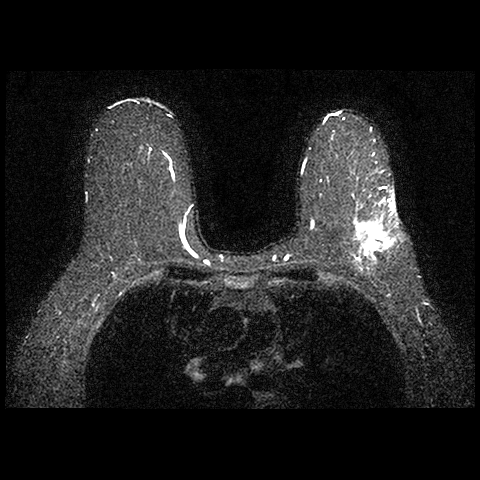
Breast MRI examination; 2 images, each one mid-volume slice chosen by position. Patient in her 70s.
Image 1: fluid-sensitive (T2/STIR) axial slice, slice 43 of 84, 2 mm slice thickness.
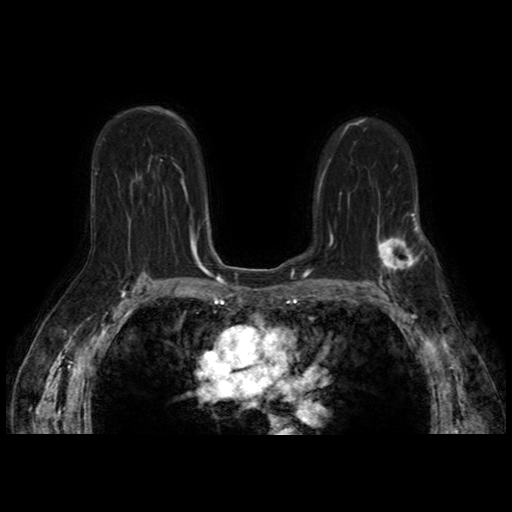
Image 2: post-contrast dynamic axial slice, series "AX BLISS_AUTO SENSE", slice 43 of 84, dynamic phase 6 of 10, 4 mm slice thickness.
MRI impression (as recorded): LEFT BREAST: There is minimal background enhancement. A mass in the left upper outer posterior breast has irregular margins with peripheral irregular enhancement and has associated mild architectural distortion. It is located at 2 o'clock , approximately 10 cm from the nipple and 2.2 cm from the chest wall. The mass demonstrates rapid intense early contrast enhancement with washout. It measures approximately 2.8 x 2.3 x 2.4 cm (Series 705, Slice 84). A biopsy clip is noted in the lateral portion of the mass. Two satellite foci of enhancement are noted adjacent to the known cancer with washout kinetics. One measures approximately 0.6 x 0.4 x 0.7 cm (Series 705, Slice 66), and is located approximately 1 cm inferior to the large mass in the left upper outer breast at 2 o'clock, approximately 10 cm from the nipple. The other focus of enhancement measures approximately 0.3 x 0.2 x 0.8 cm and is located approximately 6 mm posterior to the large mass (Series 705, Slice 76) at approximately 1 0'clock, 12.5 cm from the nipple. There are enlarged left axillary lymph nodes measuring up to 3.1 x 1.5 cm (Series 301, Slice 118). A 1.2 x 0.6 cm left subpectoral lymph node is also noted (Series 301, Slice 146), between the pectoralis minor and chest wall, just below the left subclavian vessels. No skin thickening or nipple inversion. RIGHT BREAST: There is minimal background enhancement. No foci of suspicious enhancement, masses, or areas of architectural distortion seen within the right breast. There is no skin thickening, nipple inversion, or right axillary lymphadenopathy present. IMPRESSION: 1) Approximately 2.8 cm mass in the left upper outer breast, biopsy proven cancer, with two adjacent satellite foci measuring up to 0.8 cm. 2) Enlarged metastatic left axillary lymph nodes and a left subpectoral - subclavian lymph node. 3) No evidence of malignancy in the right breast; BI-RADS 6.
Pathology recorded for this patient (not read from these images): receptor status (as recorded): ER pos (strong), PR pos (strong), HER2 neg; Ki-67 (as recorded): pos (high prolif rate); pathology report notes: INFILTRATING DUCTAL CARCINOMA, MODIFIED SCARFF-BLOOM-RICHARDSON GRADE-II/III. NO INTRADUCTAL CARCINOMA COMPONENT.